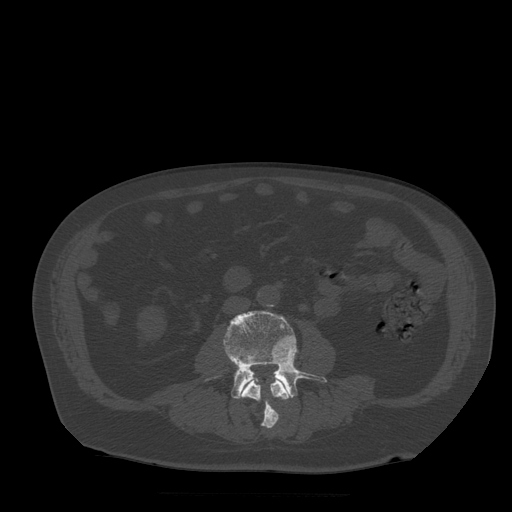
CT including the spine, one axial slice. Slice 125 of 522 in the series (ordered by position). Bone window (W 1800 / L 400 HU). 1.25 mm slice thickness. 512 × 512 image matrix. Patient age 72 years. From the clinical record (not read from this slice): primary cancer: prostate.
Annotated regions visible in this slice (semi-automatically segmented with operator editing):
- L3 vertebra: box from (x=240, y=380) to (x=290, y=429) px
- L4 vertebra: (x=223, y=311)–(x=327, y=399)